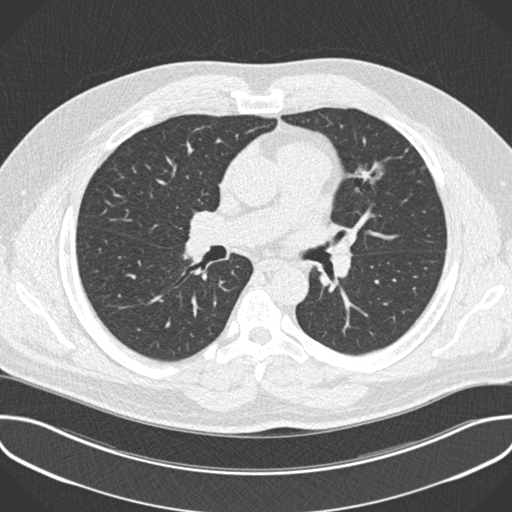
Low-dose screening chest CT, one axial slice. Slice 123 of 201 in the series (ordered by position). 120 kVp. Lung window (W 1500 / L -600 HU). 2 mm slice thickness. 512 × 512 image matrix, field of view 386 × 386 mm.
Outlined on this slice (outlined manually by an expert reader):
- lesion 1 (tumor, upper lobe of left lung): bounding box <357,169,373,179> (left, top, right, bottom; pixels)